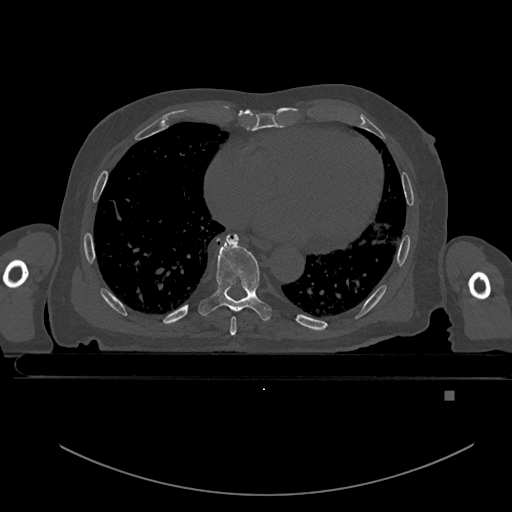
CT including the spine, one axial slice; slice 207 of 969 in the series (ordered by position); bone window (W 1800 / L 400 HU); 0.5 mm slice thickness; 512 × 512 image matrix, field of view 456 × 456 mm. Patient: male, 82 years. From the clinical record (not read from this slice): primary cancer: prostate; vertebrae with lytic lesions (as recorded): T11, T9, T8, T2.
Outlined on this slice (semi-automatic segmentation, software-assisted and operator-edited):
- T7 vertebra: bounding box <230,317,236,335> (left, top, right, bottom; pixels)
- T8 vertebra: <198,234,272,321>